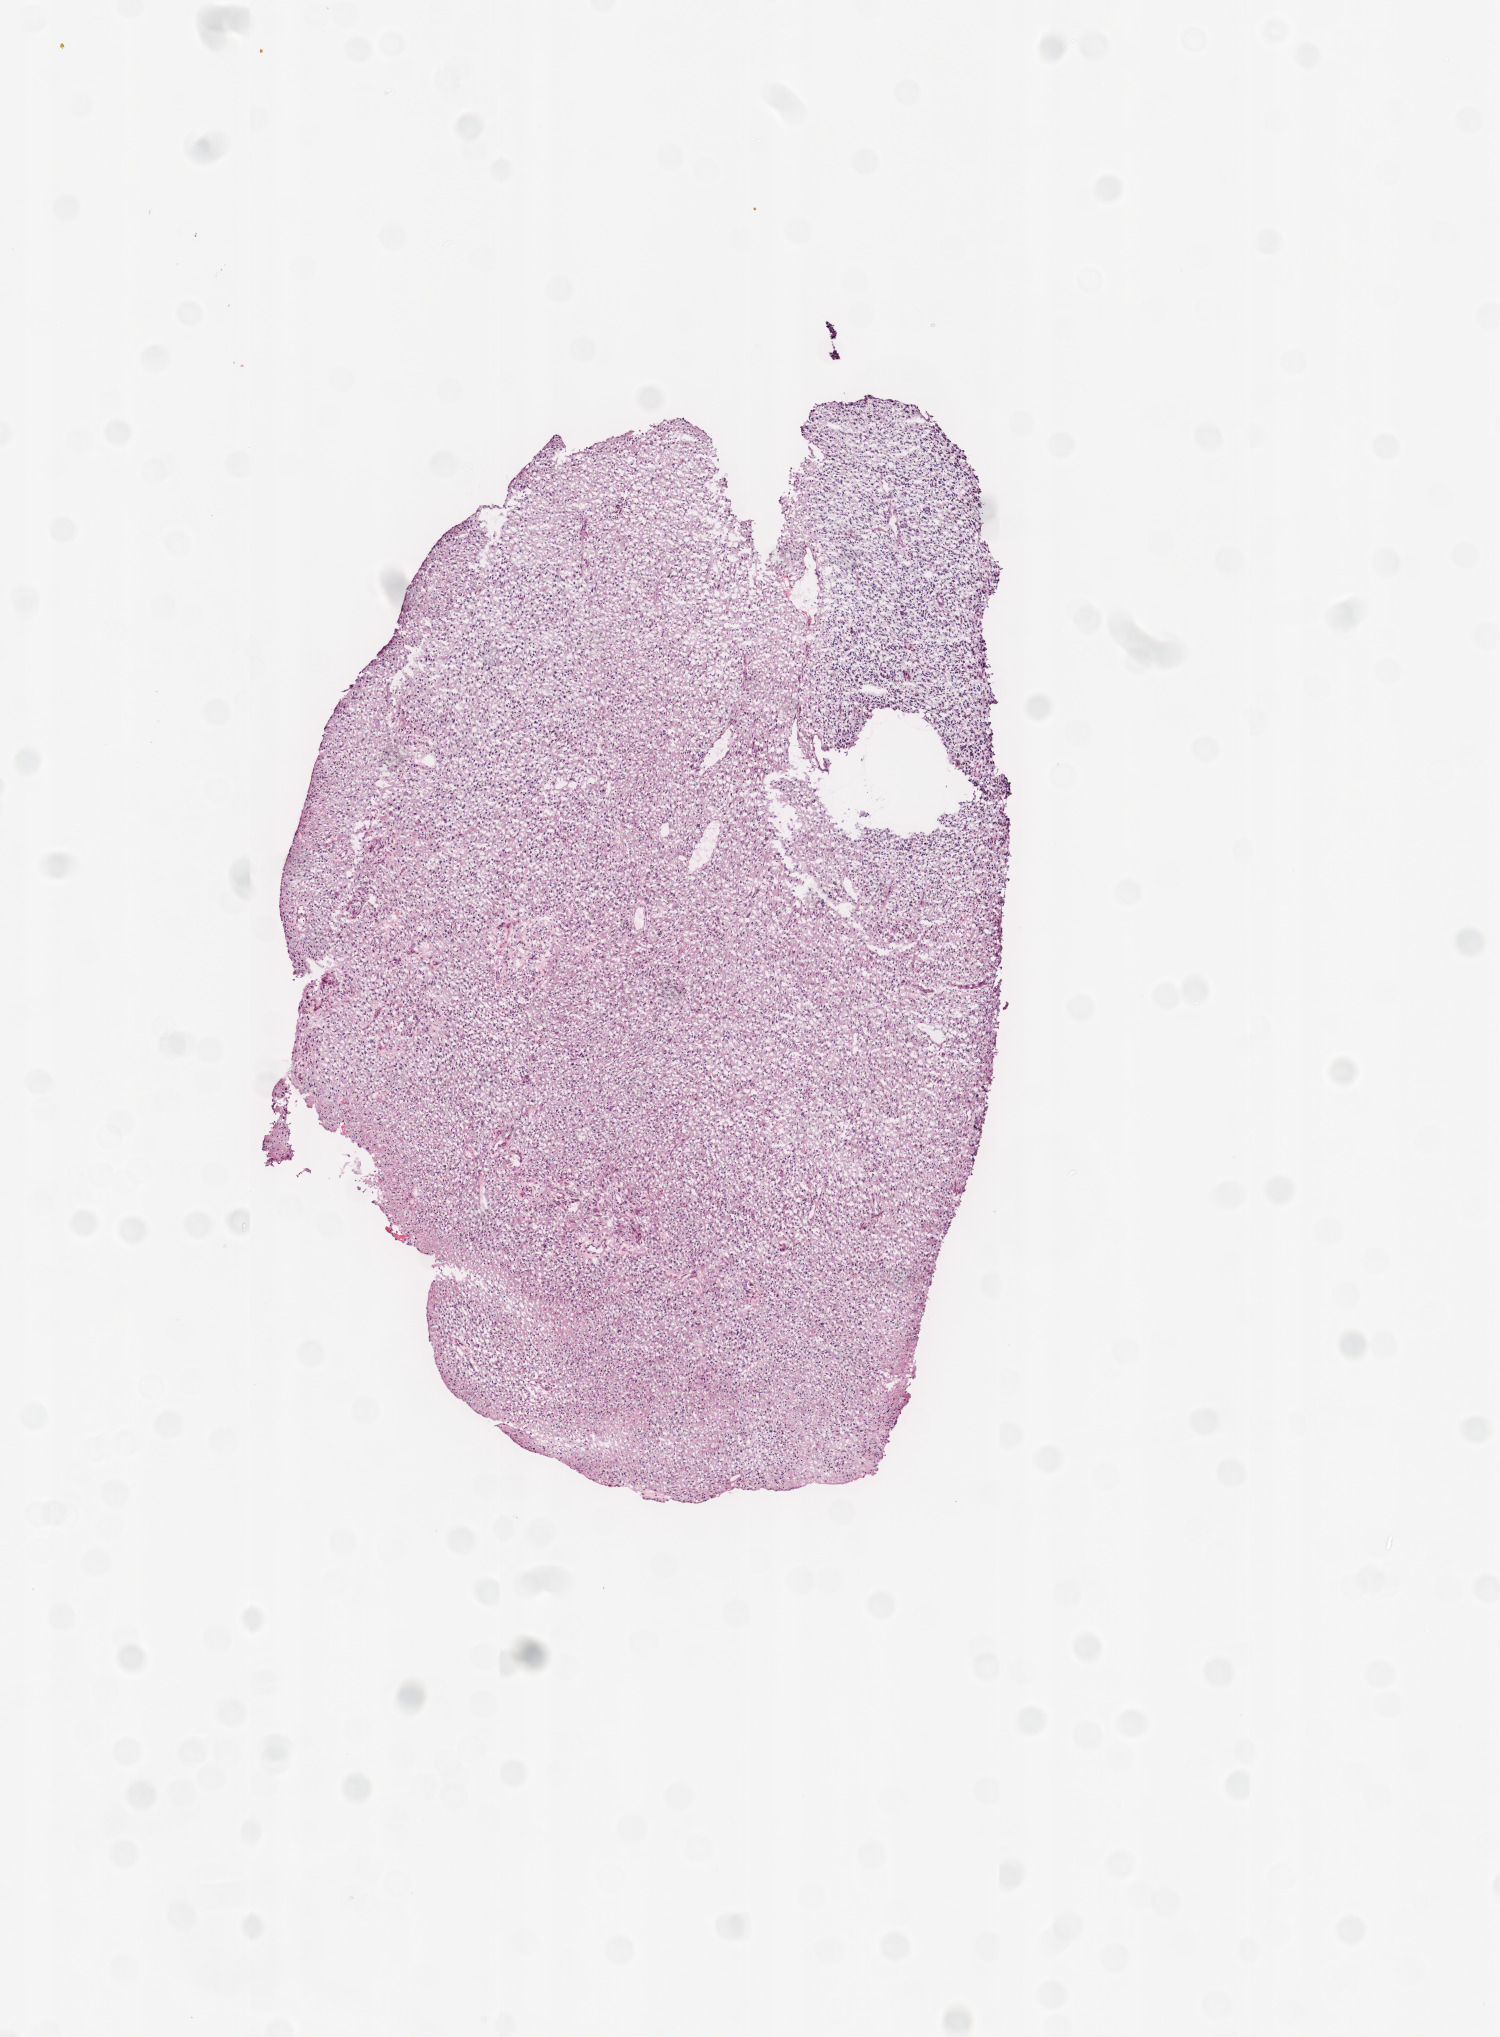
Hematoxylin and eosin (H&E) stained whole-slide image — whole scanned area (about 6.0 x 8.2 mm, from a 20x scan) shown as a low-resolution overview, frozen section from the top of the tissue portion, brain, primary tumour sample. Patient: male, age at initial diagnosis 65 years. Composition of this section per pathologist review: tumour cells 98%, tumour nuclei 85%, normal cells 0%, stromal cells 0%, necrosis 2%.
• pathologic diagnosis: Glioblastoma